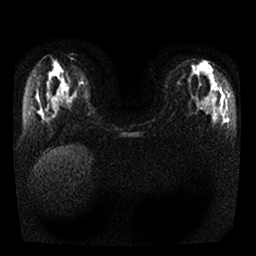
Breast MRI, one axial slice; position 14 of 25 along the scan axis; diffusion-weighted series; image 2 of 4 stored at this slice position (different b-values; order by instance number); 1.5 T; 4 mm slice thickness; 256 × 256 image matrix, field of view 320 × 320 mm. Female patient.
Annotated regions visible in this slice (manually delineated by an expert):
- tumour on diffusion-weighted imaging: box from (x=206, y=108) to (x=210, y=113) px